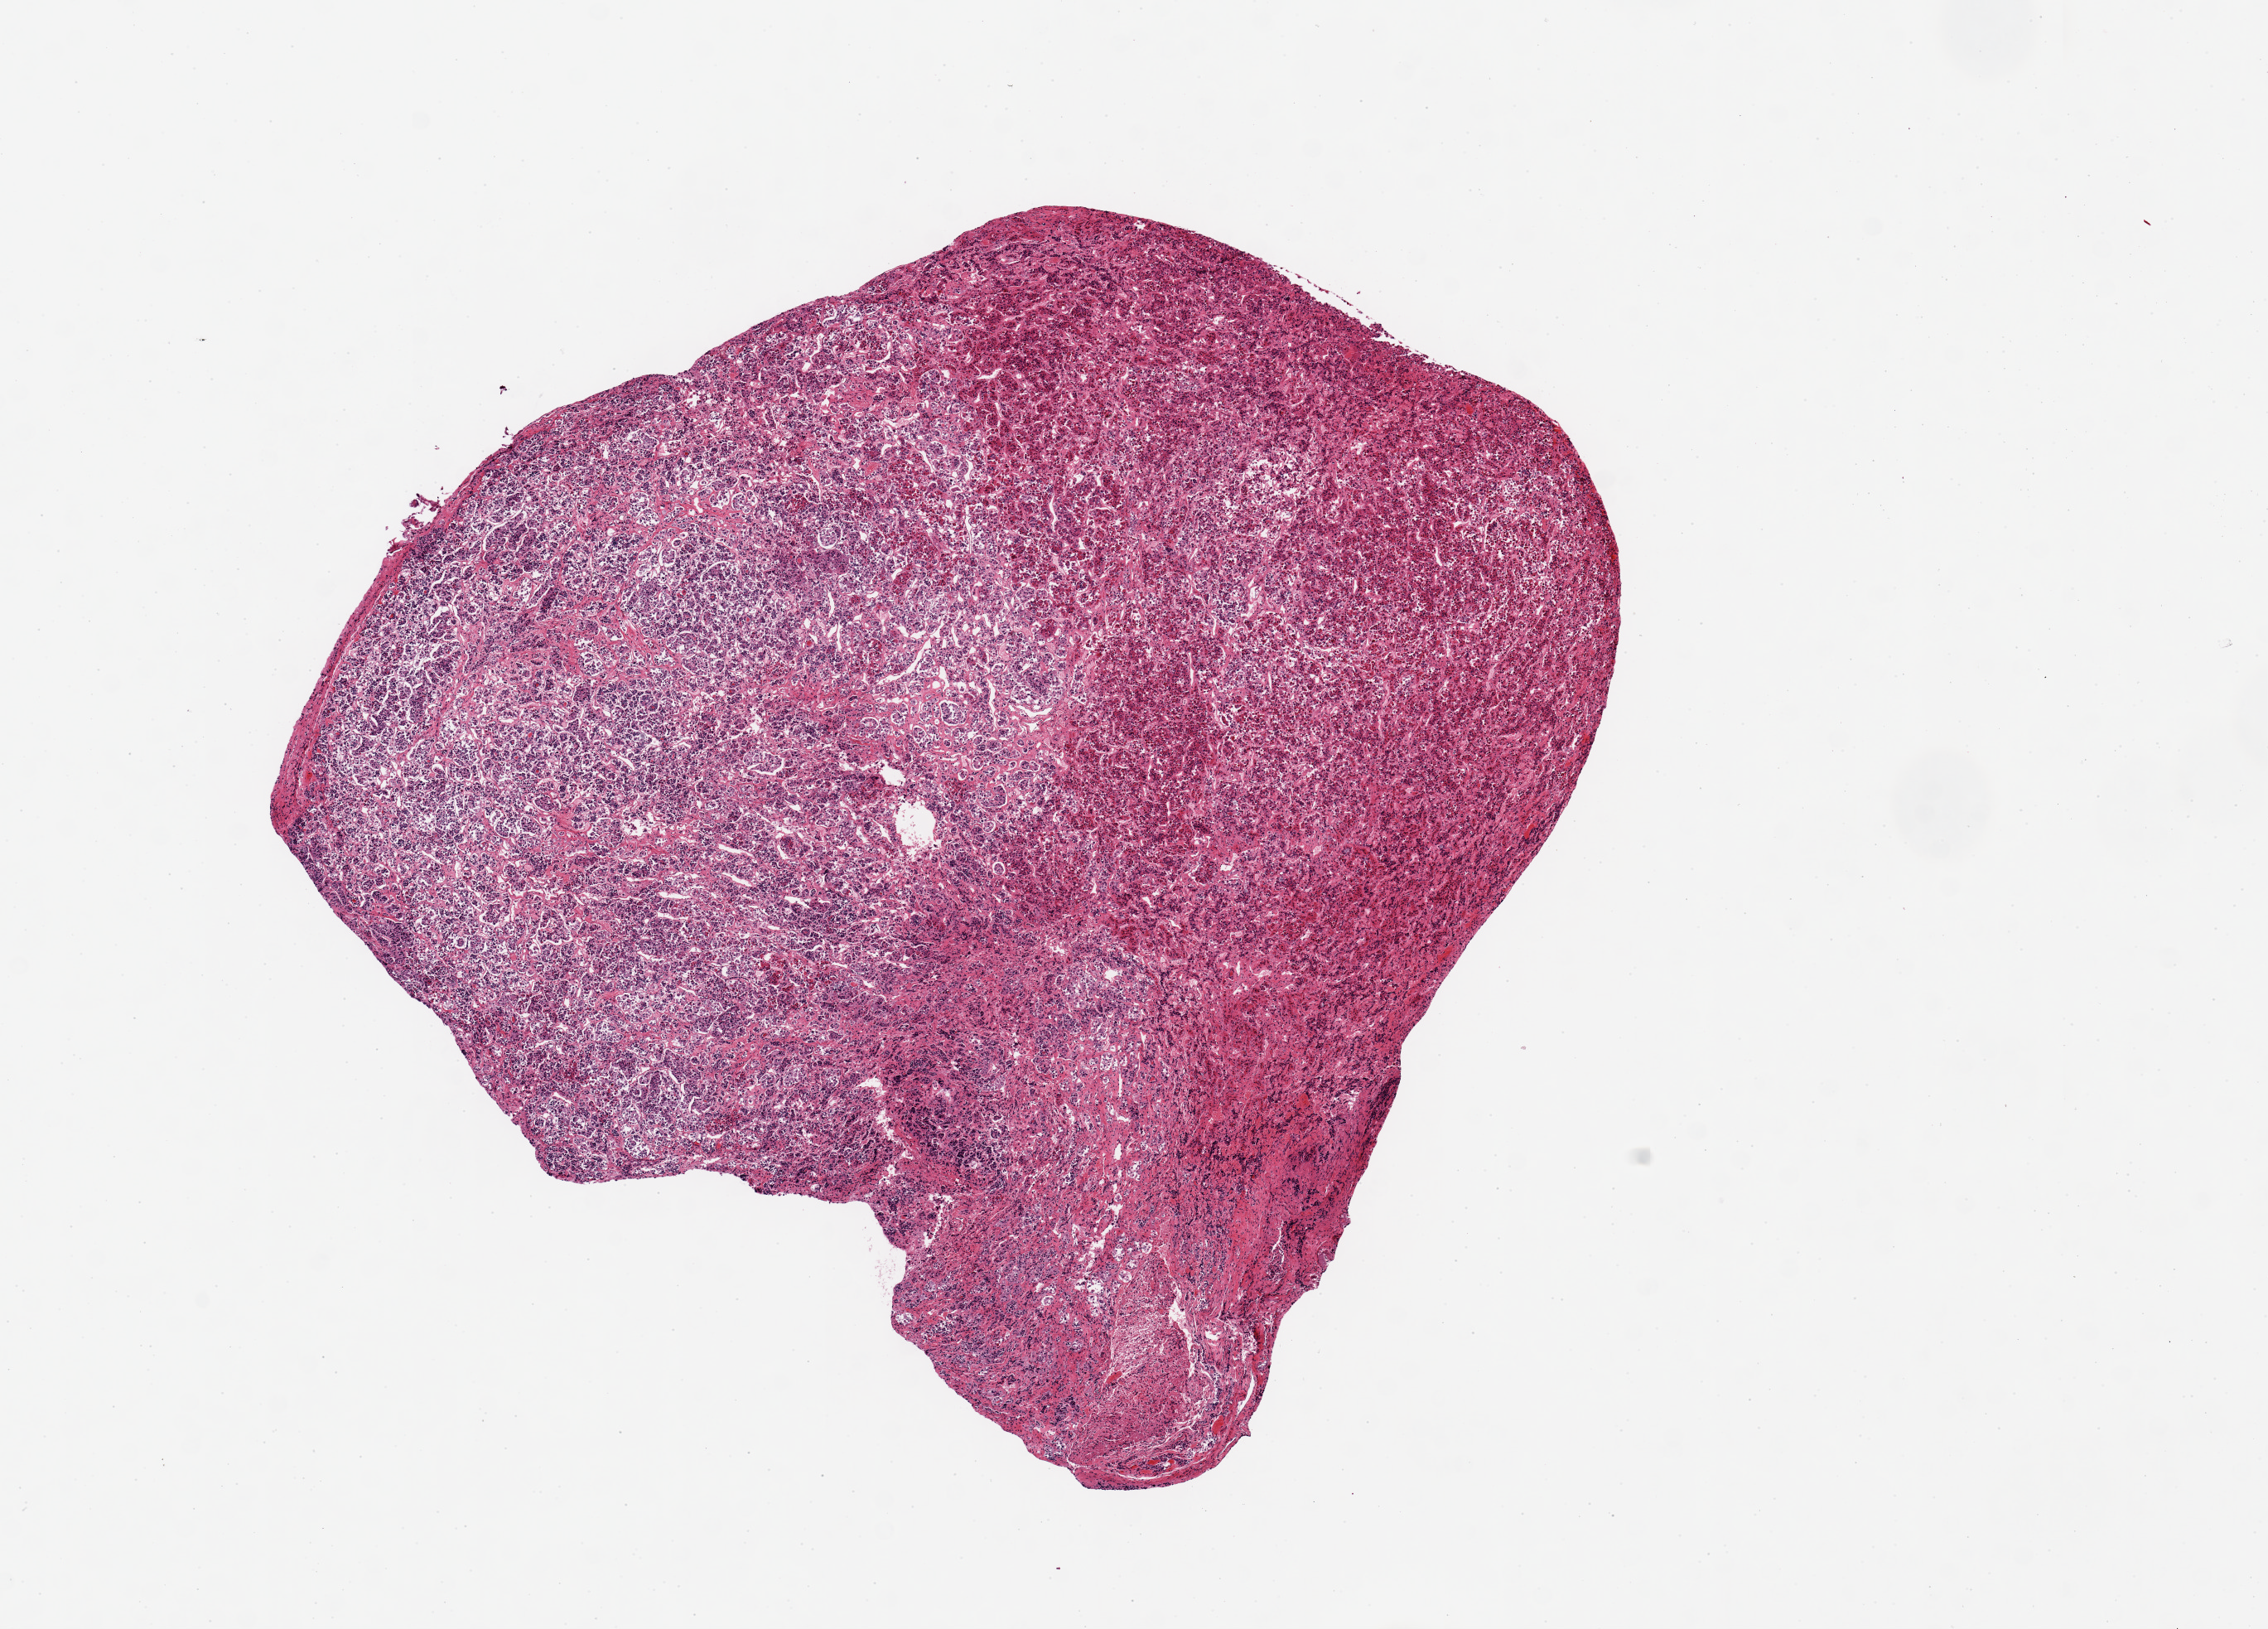
Whole-slide image, haematoxylin and eosin stain, brightfield — a low-resolution overview of the entire scanned area, about 10.8 x 7.8 mm. PAXgene-fixed paraffin-embedded (PFPE) section. Target tissue: pituitary. Tissue donor sample. Male donor.
Pathologist's review note for this sample: 1 piece 5x5 mm; anterior.